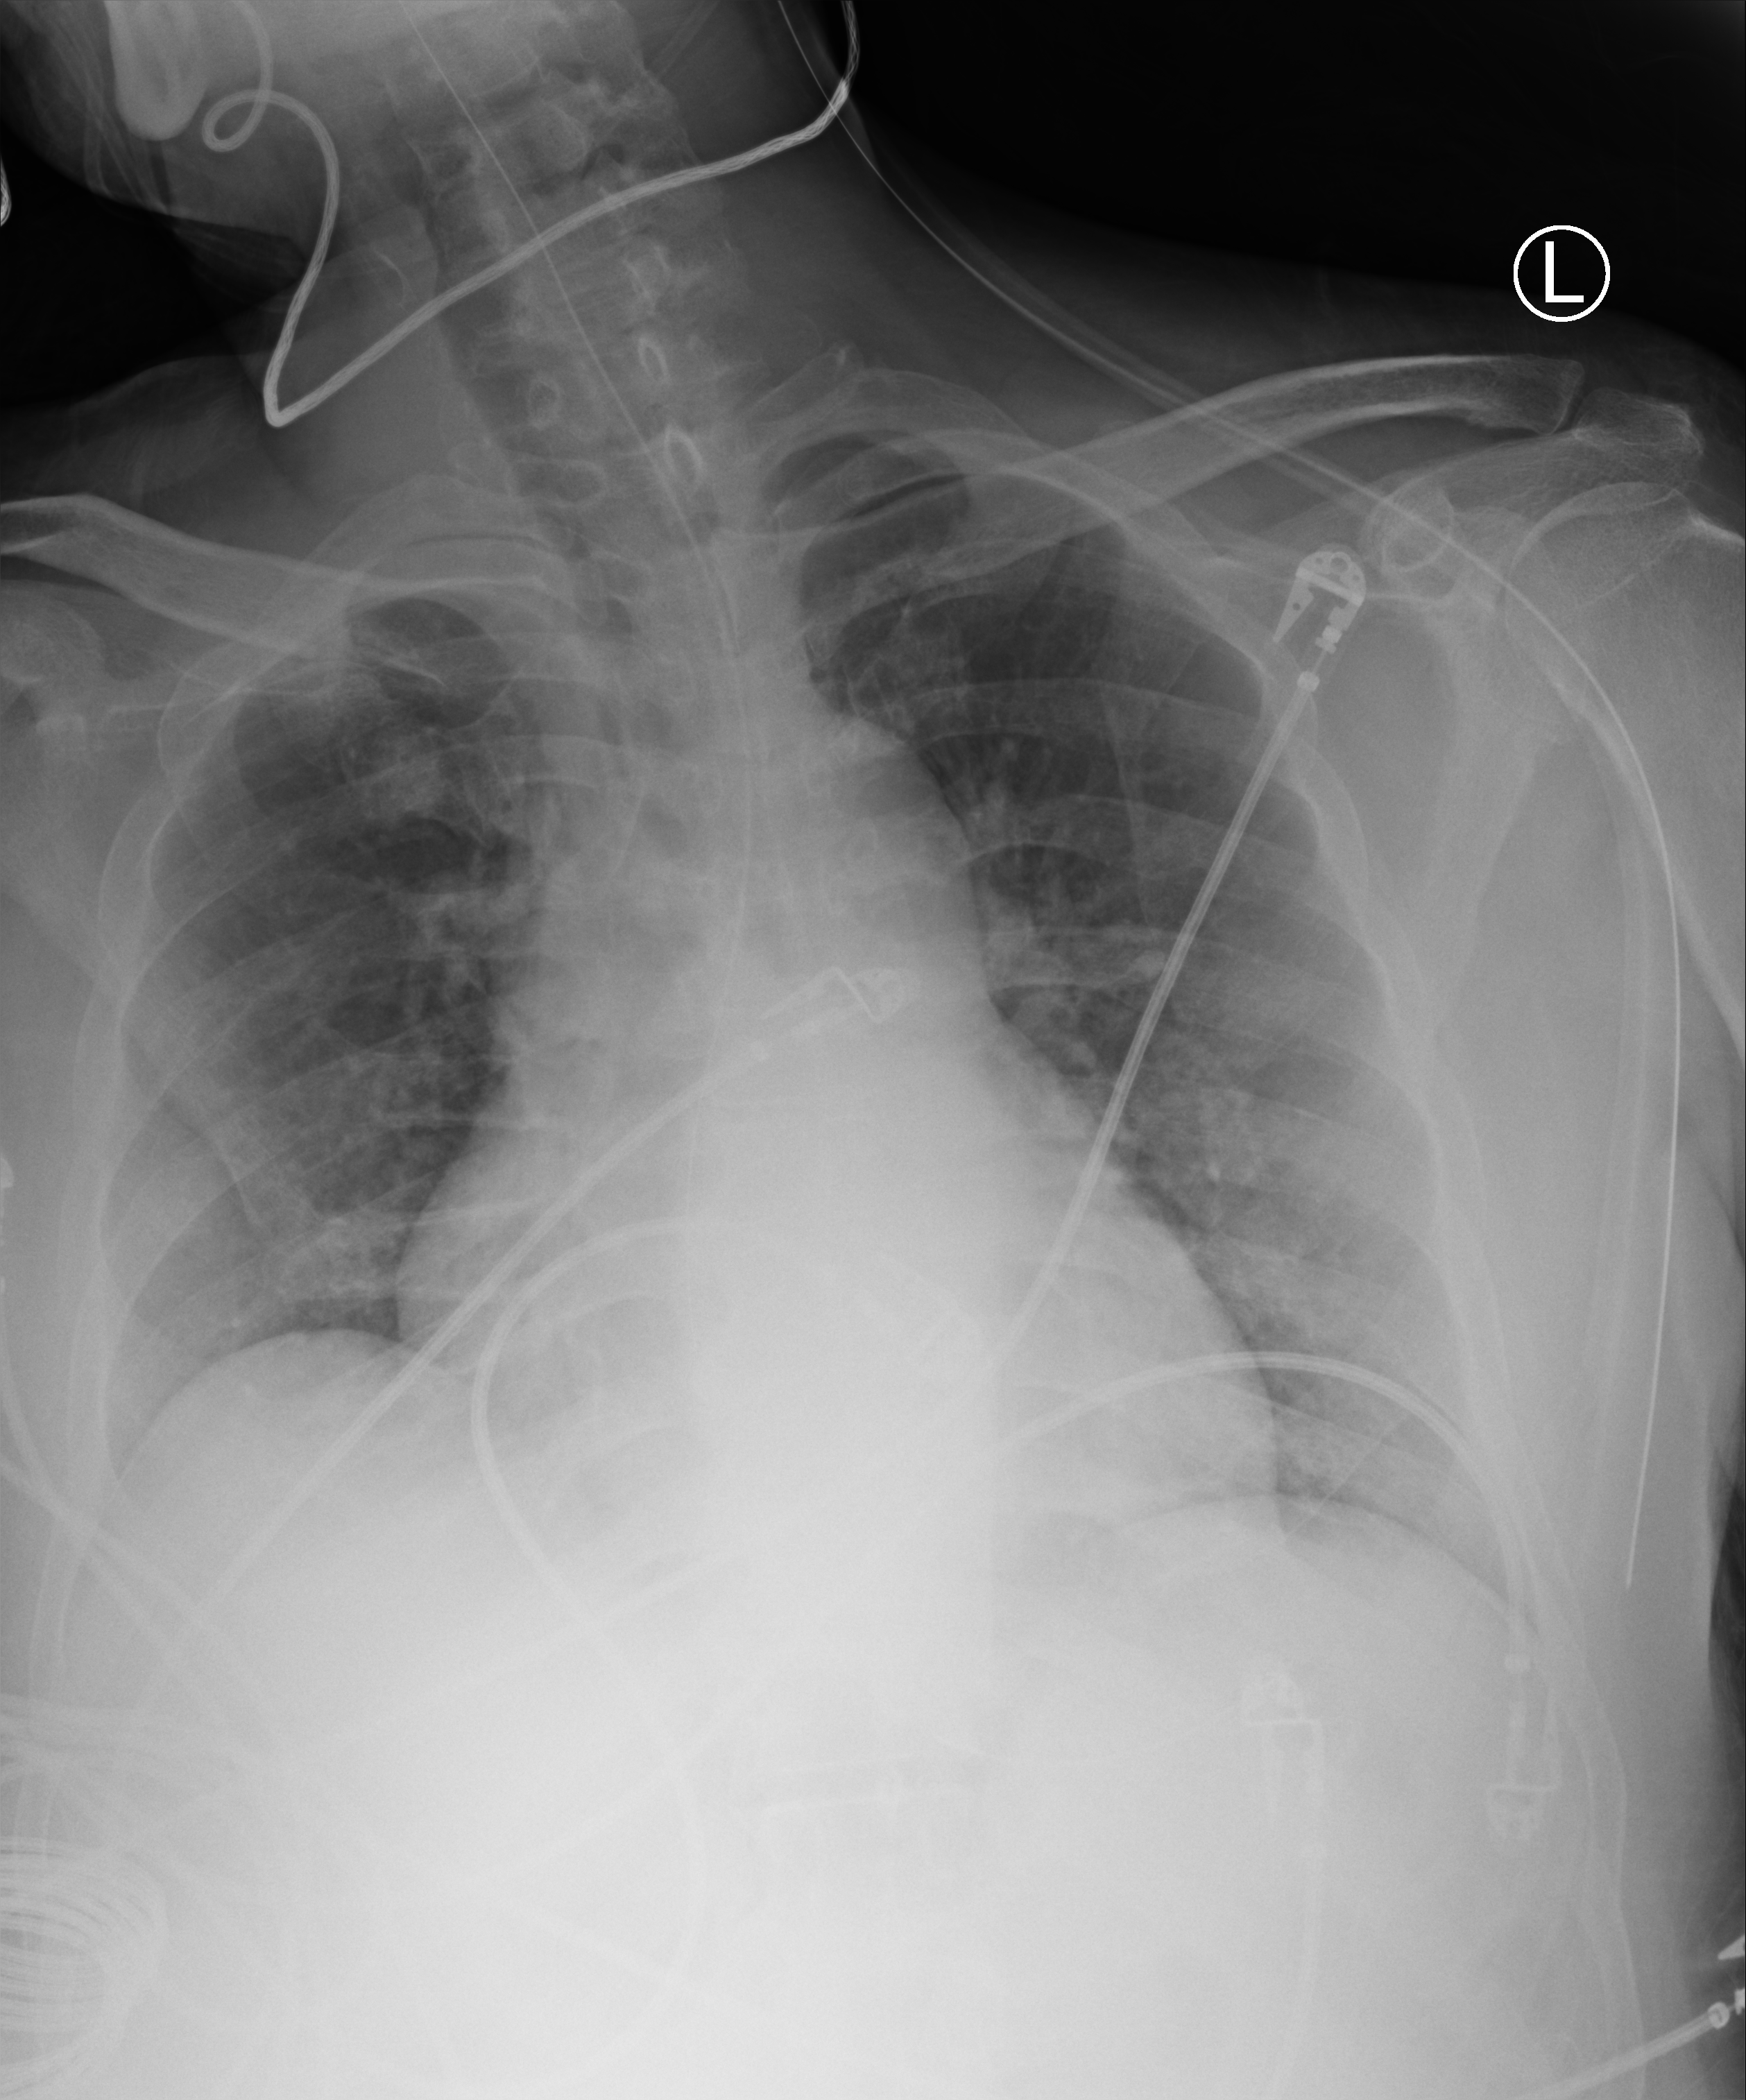
Chest X-ray (portable). Adult patient hospitalised with COVID-19, age 18–59 years.
Hospital-stay facts (about this admission, not read from this image; timing relative to this image not recorded): COPD (admission record): no; admitted to intensive care during this hospital stay: yes; other chronic lung disease (admission record): no.